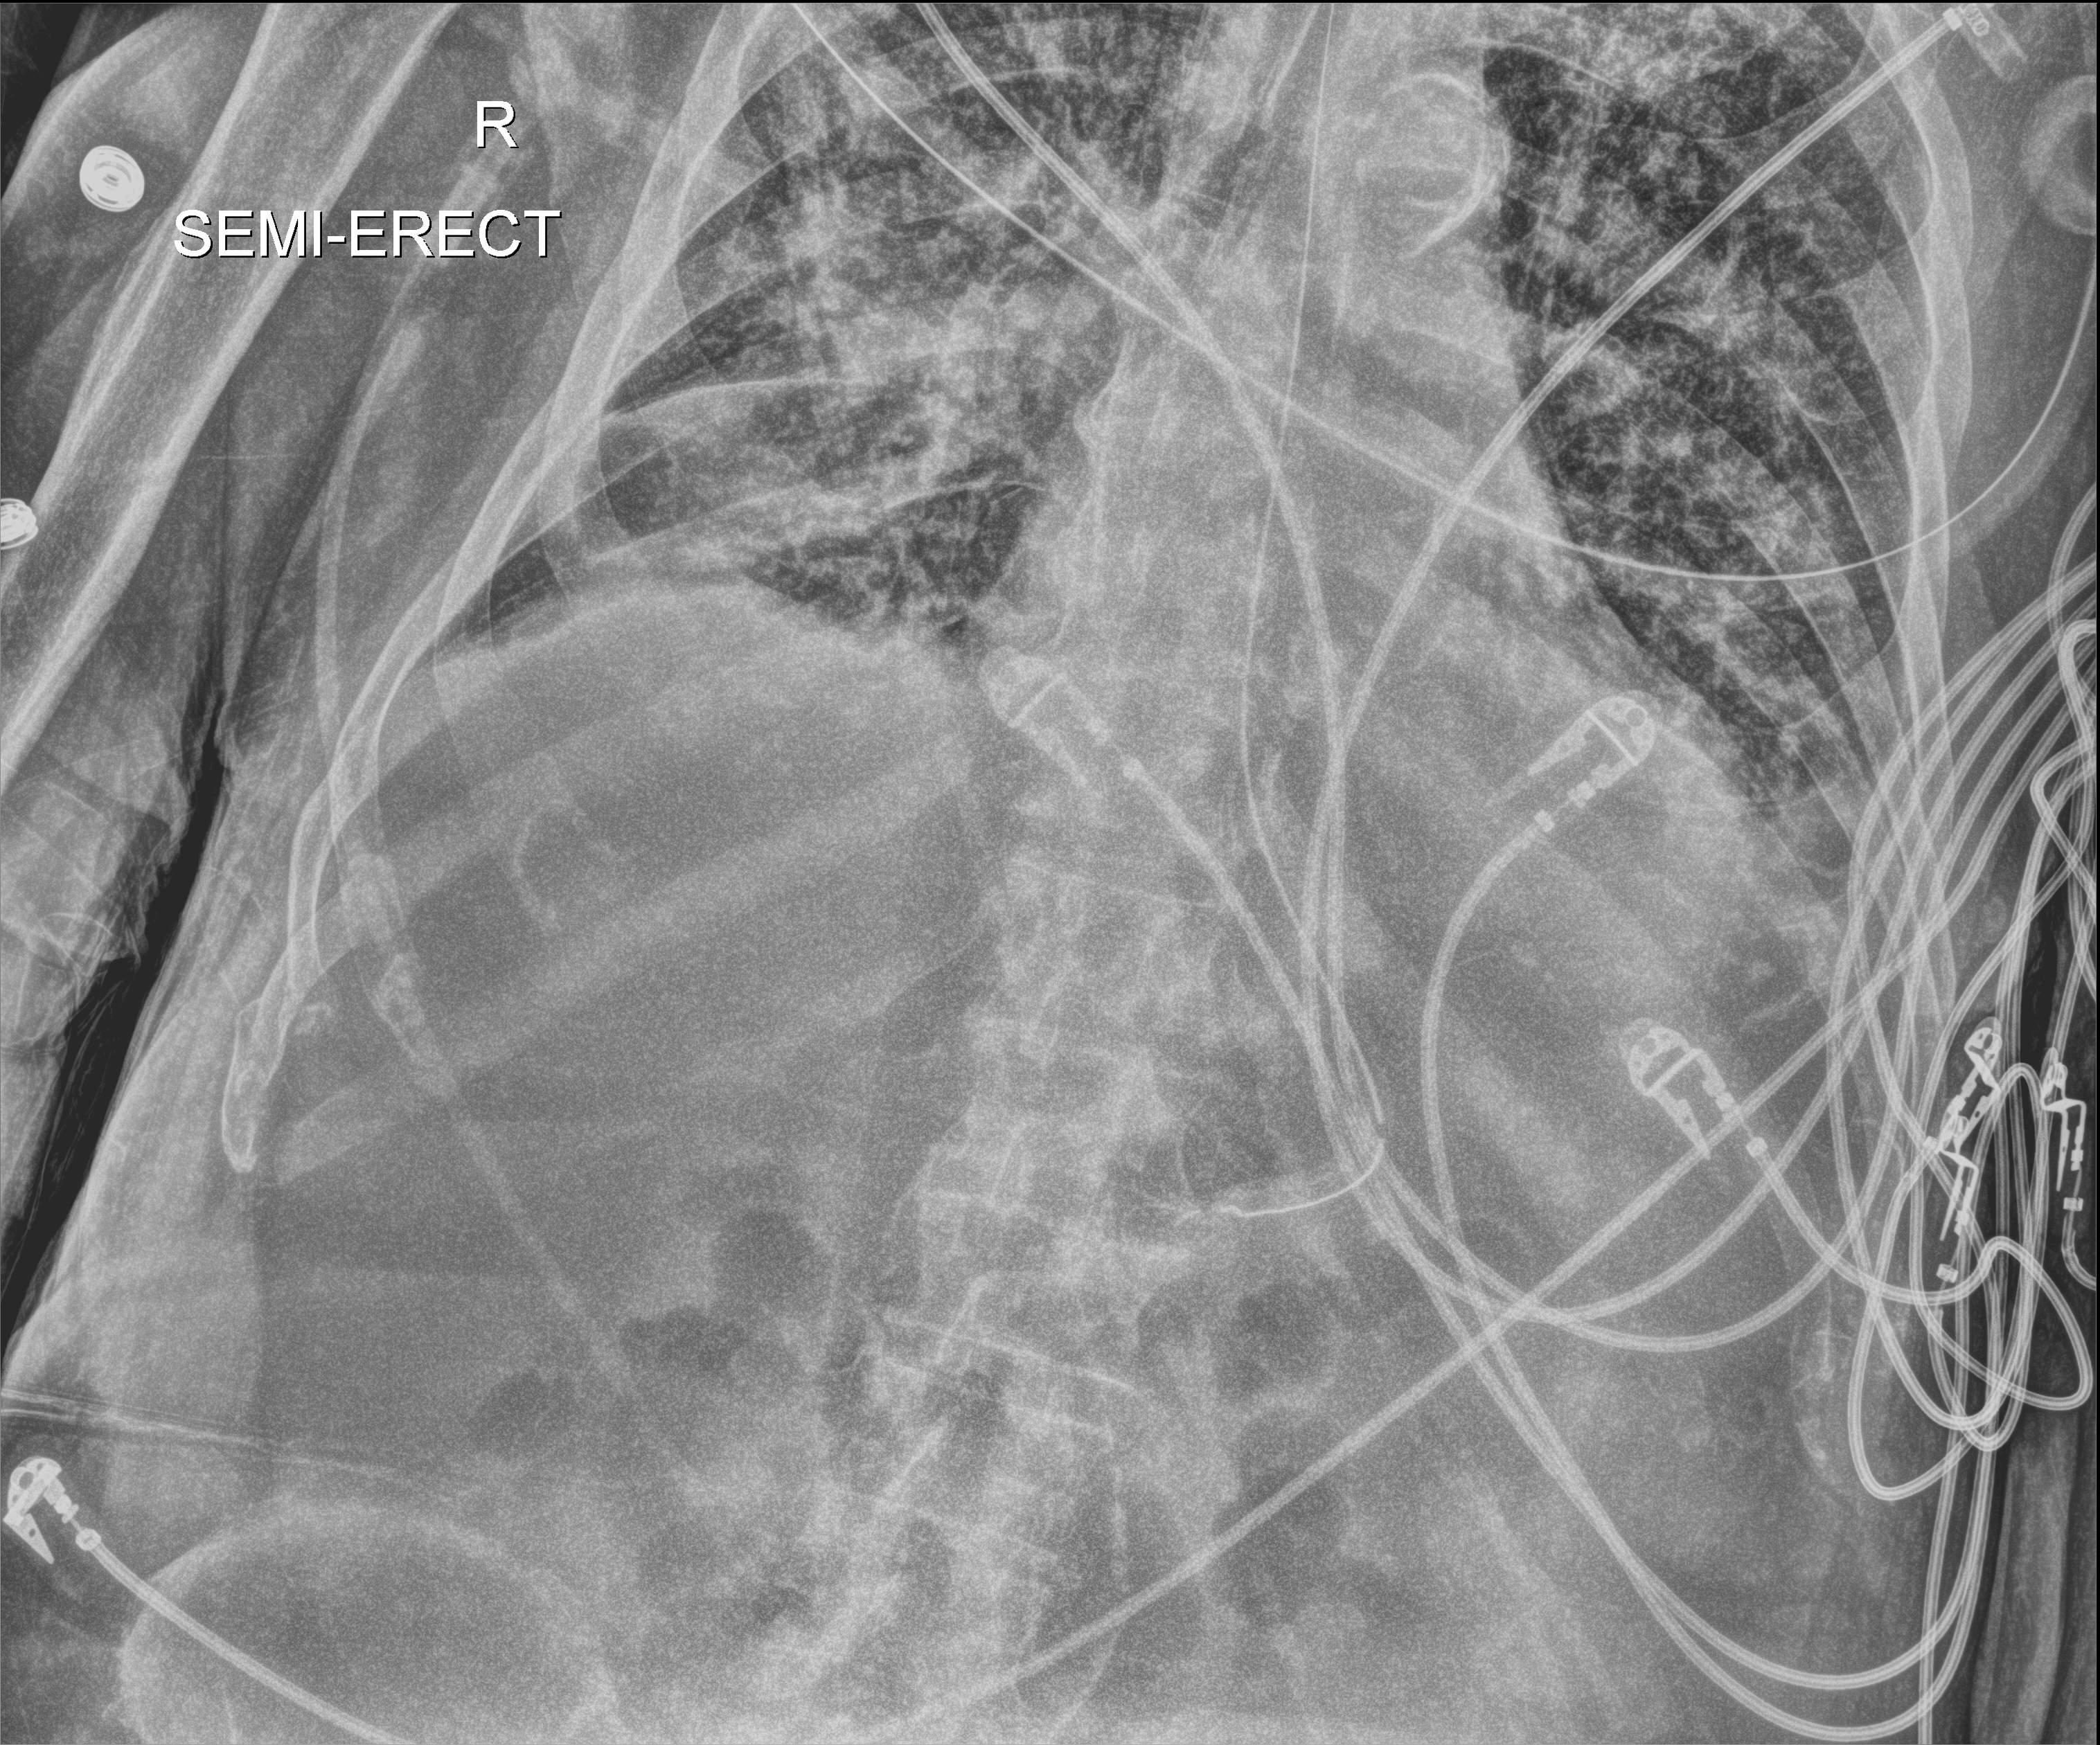
Bedside chest radiograph (digital radiography). Male patient hospitalised with COVID-19, age 75–90 years.
From the hospital-stay record, not from the radiograph (when in the stay this image was taken is not recorded):
- admitted to intensive care during this hospital stay: yes
- mechanically ventilated during this hospital stay: yes
- smoking status (admission record): never